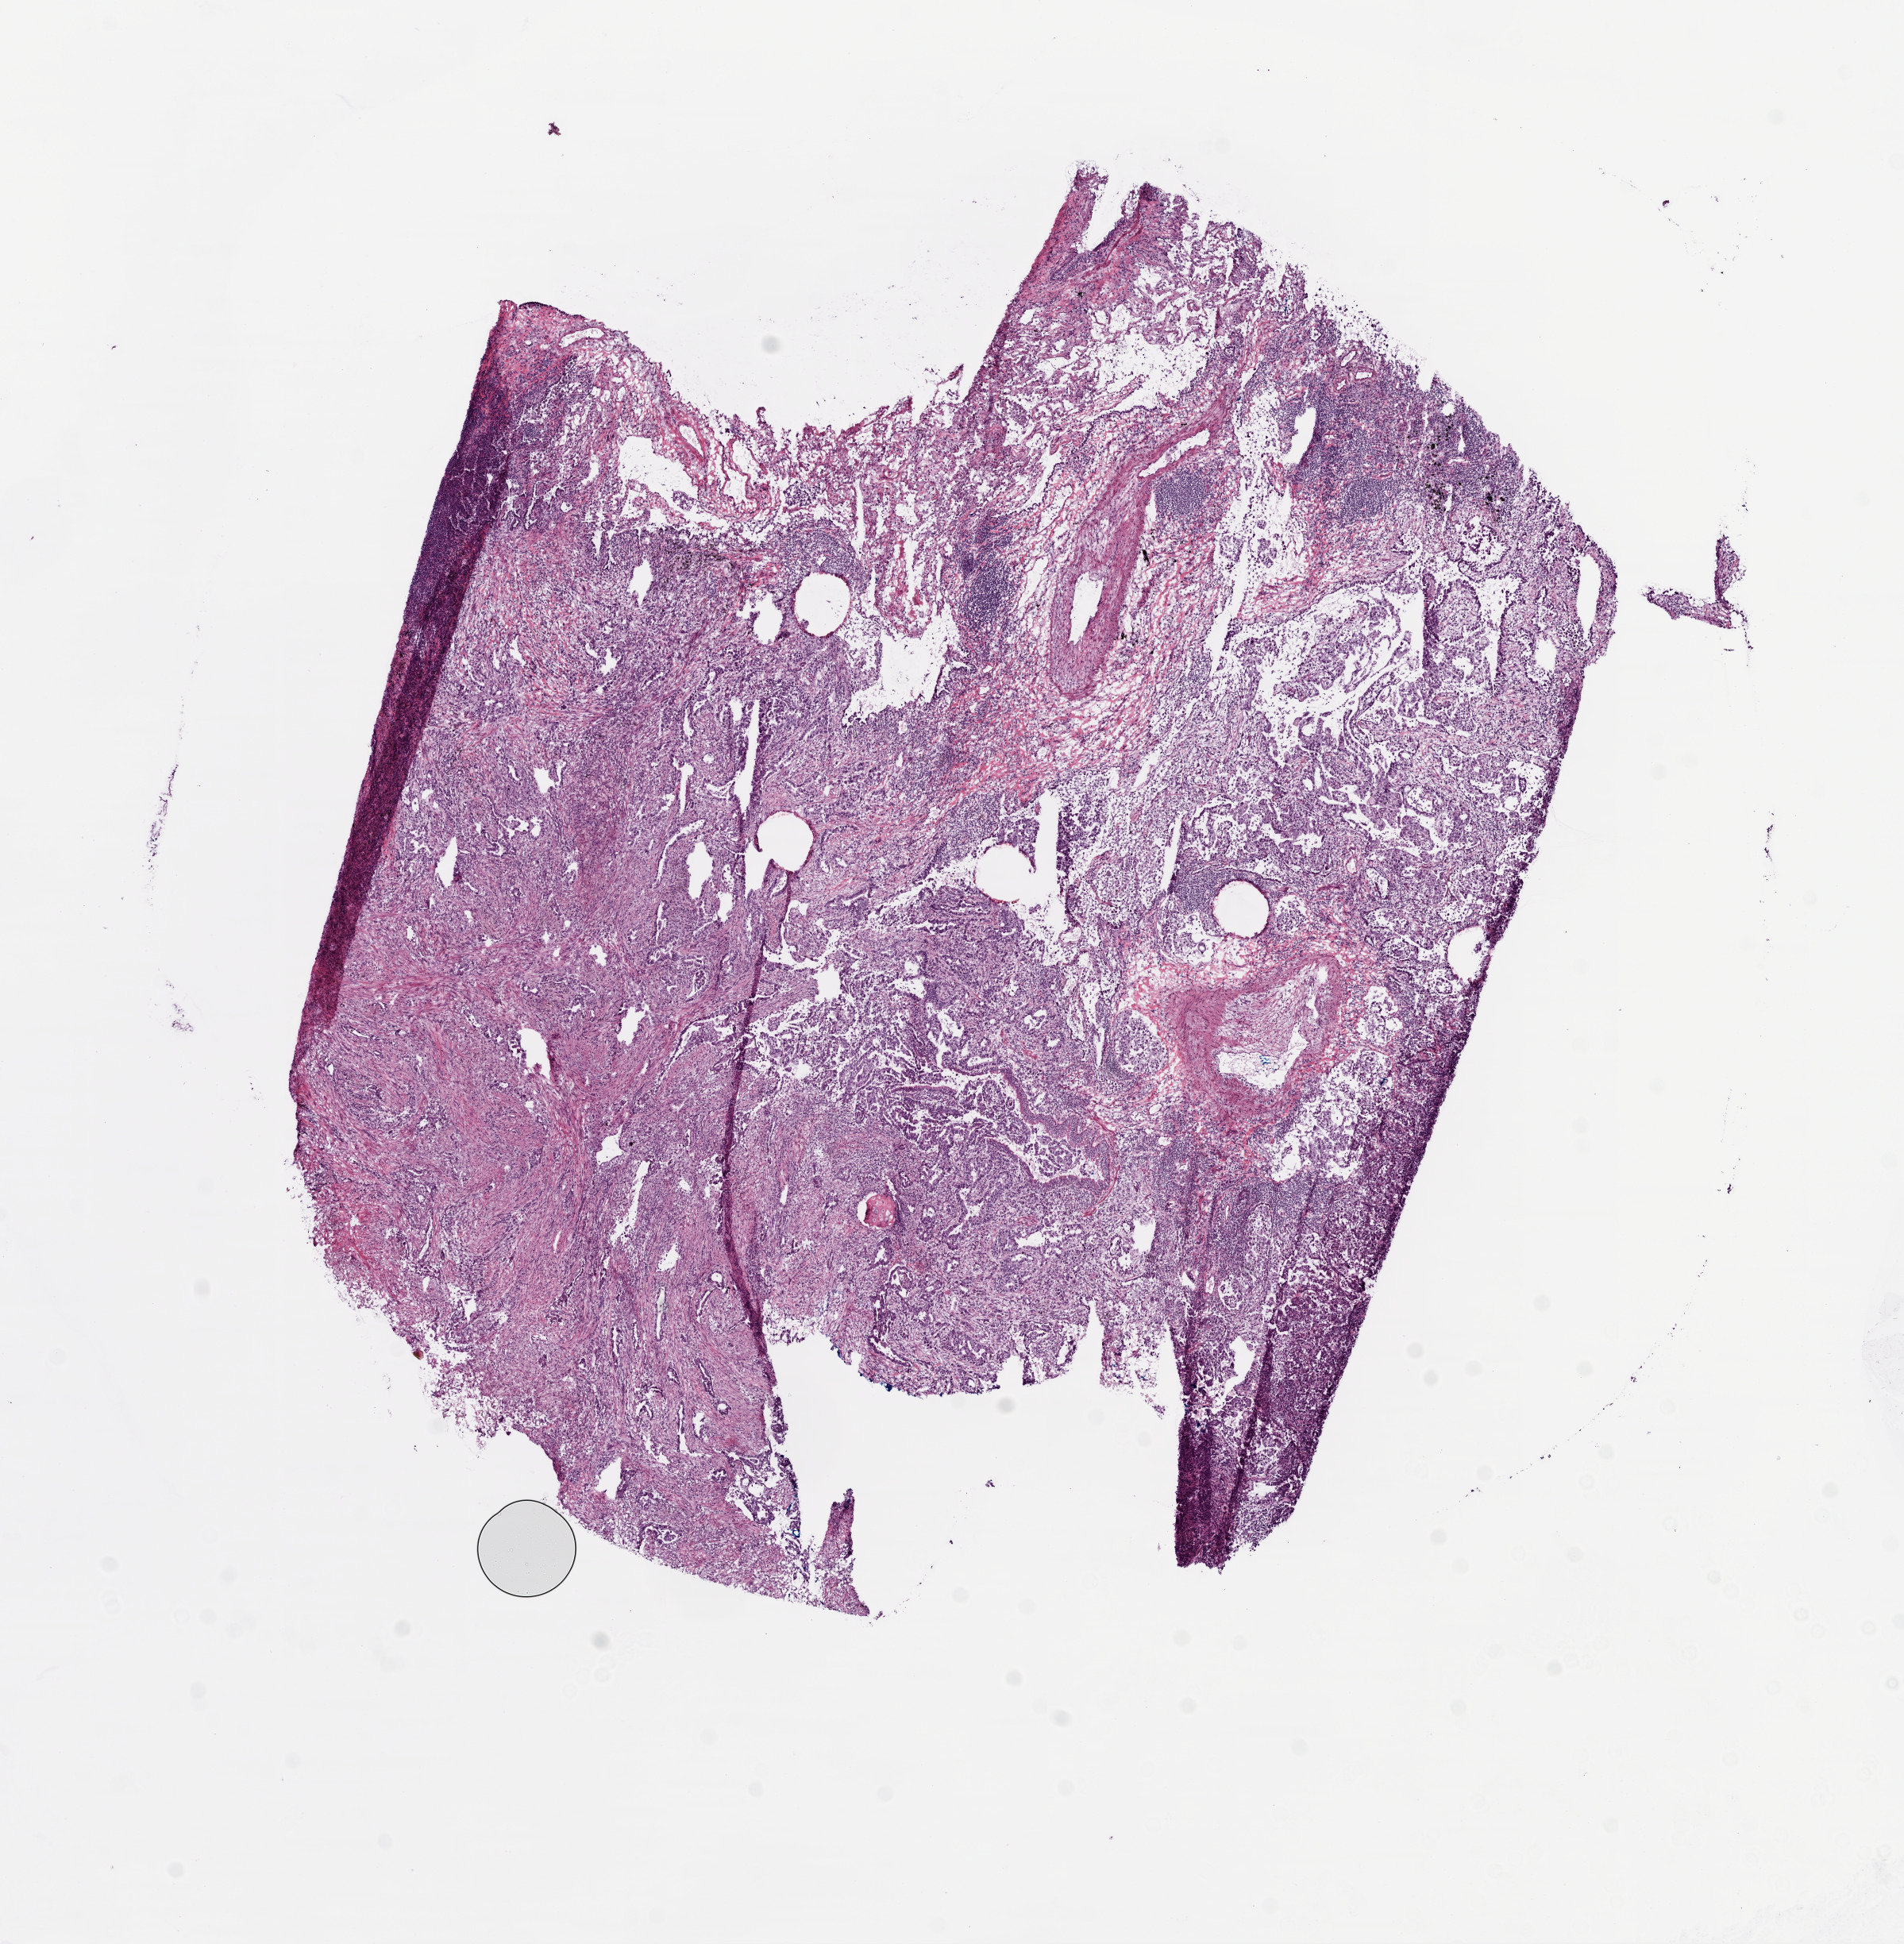
Digitized H&E tissue section (whole slide) — shown as a low-resolution overview of the whole scanned area (about 9.7 x 9.9 mm). Frozen section from the top of the tissue portion. Sample: primary tumour, lung. Patient: female, age at initial diagnosis 58 years. Pathologist review of this section (percent, as recorded): tumour cells 70%, tumour nuclei 60%, normal cells 0%, stromal cells 30%, necrosis 0%.
TNM: T2 N0 MX. Pathologic diagnosis: Adenocarcinoma, NOS (upper lobe, lung). AJCC pathologic stage: IB (6th edition). Laterality: left.